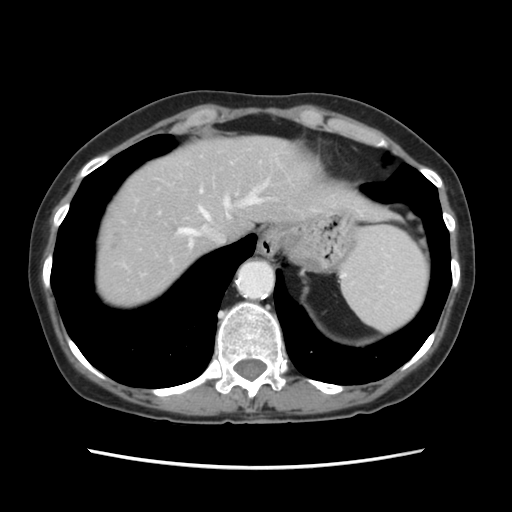
Contrast-enhanced abdominal CT, one axial slice; slice 101 of 120 in the series (ordered by position); intravenous contrast given; soft-tissue window (W 400 / L 40 HU); 2.5 mm slice thickness; 512 × 512 image matrix, field of view 330 × 330 mm. Female patient, age 70 years. Case-level facts recorded for this patient, not image findings: diagnosis: colorectal cancer liver metastases, imaged before liver resection; multiple liver metastases: no; largest metastasis: 2.5 cm.
Outlined on this slice (outlined manually by an expert reader):
- hepatic veins: box from (x=180, y=191) to (x=260, y=245) px
- liver: (x=96, y=138)–(x=343, y=303)
- planned liver remnant (the part of the liver to remain after resection): (x=148, y=137)–(x=343, y=257)
- portal vein (with intrahepatic branches): (x=200, y=190)–(x=202, y=193)
- liver metastasis: (x=113, y=234)–(x=122, y=245)